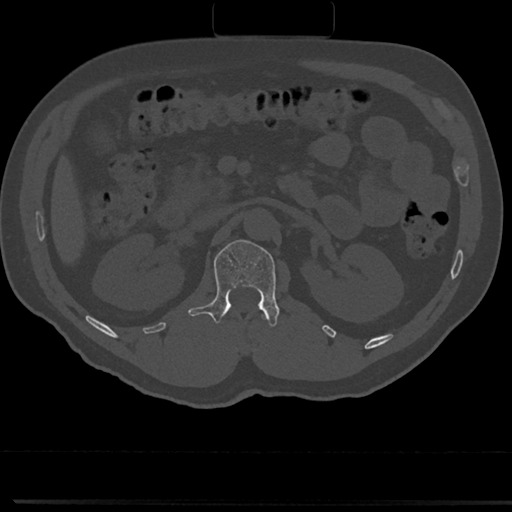
CT including the spine, one axial slice. Position 93 of 817 along the scan axis. 120 kVp. Bone window (W 1800 / L 400 HU). 0.5 mm slice thickness. 512 × 512 image matrix, field of view 355 × 355 mm. Patient: male, 61 years. Case-level facts recorded for this patient, not image findings: primary cancer: prostate.
Structures marked on this image (semi-automatically segmented with operator editing):
- L1 vertebra: box from (x=191, y=239) to (x=281, y=326) px